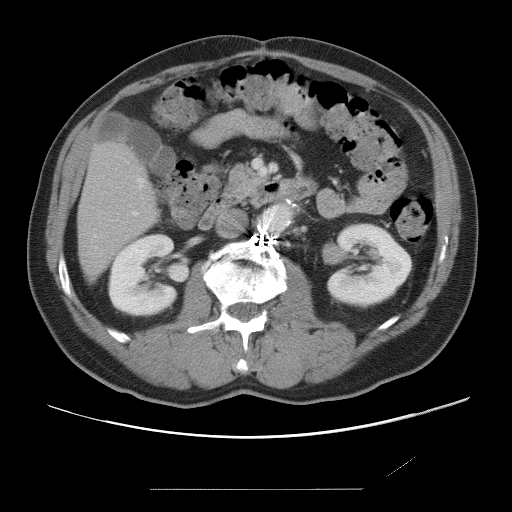
Contrast-enhanced abdominal CT, one axial slice; position 23 of 87 along the scan axis; soft-tissue window (W 400 / L 40 HU); 512 × 512 image matrix, field of view 406 × 406 mm. Male patient, age 74 years. From the clinical record (not read from this slice): diagnosis: colorectal cancer liver metastases, imaged before liver resection; multiple liver metastases: yes; largest metastasis: 1.1 cm; chemotherapy before resection: yes.
Outlined on this slice (manually delineated by an expert):
- hepatic veins: box from (x=94, y=178) to (x=143, y=237) px
- liver: (x=78, y=144)–(x=154, y=276)
- planned liver remnant (the part of the liver to remain after resection): (x=78, y=144)–(x=154, y=276)
- portal vein (with intrahepatic branches): (x=133, y=212)–(x=137, y=216)